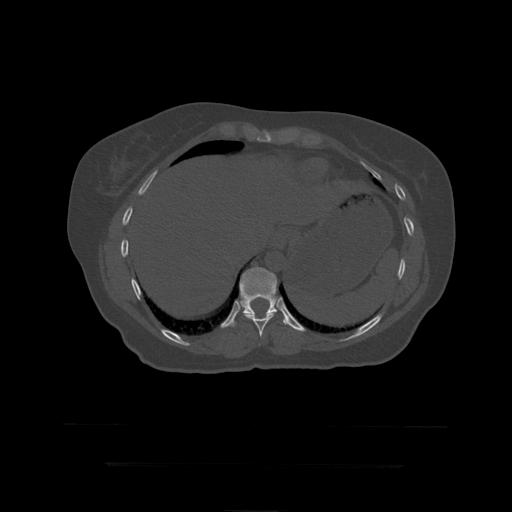
CT including the spine, one axial slice; position 232 of 399 along the scan axis; bone window (W 1800 / L 400 HU); 512 × 512 image matrix. Patient age 41 years. From the clinical record (not read from this slice): primary cancer: breast.
Outlined on this slice (semi-automatically segmented with operator editing):
- T10 vertebra: bounding box <244,313,275,337> (left, top, right, bottom; pixels)
- T11 vertebra: <230,268,290,327>